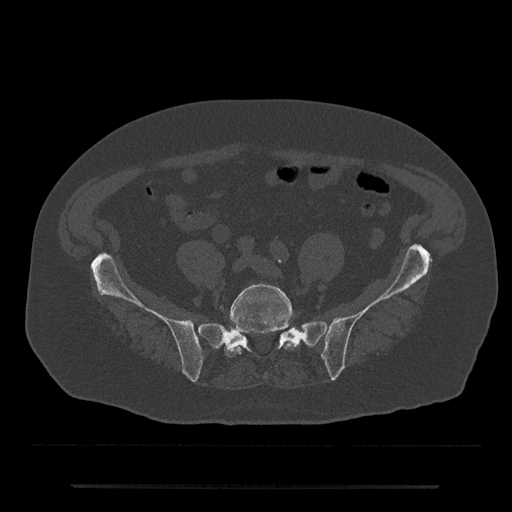
CT including the spine, one axial slice; position 263 of 797 along the scan axis; reconstruction kernel Br40s/3; bone window (W 1800 / L 400 HU); 0.5 mm slice thickness; 512 × 512 image matrix, field of view 434 × 434 mm. Patient: male, 80 years. From the clinical record (not read from this slice): primary cancer: prostate; vertebrae with lytic lesions (as recorded): L1, T11.
Annotated regions visible in this slice (semi-automatic segmentation, software-assisted and operator-edited):
- L5 vertebra: bounding box [x1, y1, x2, y2] px = [224, 283, 295, 357]